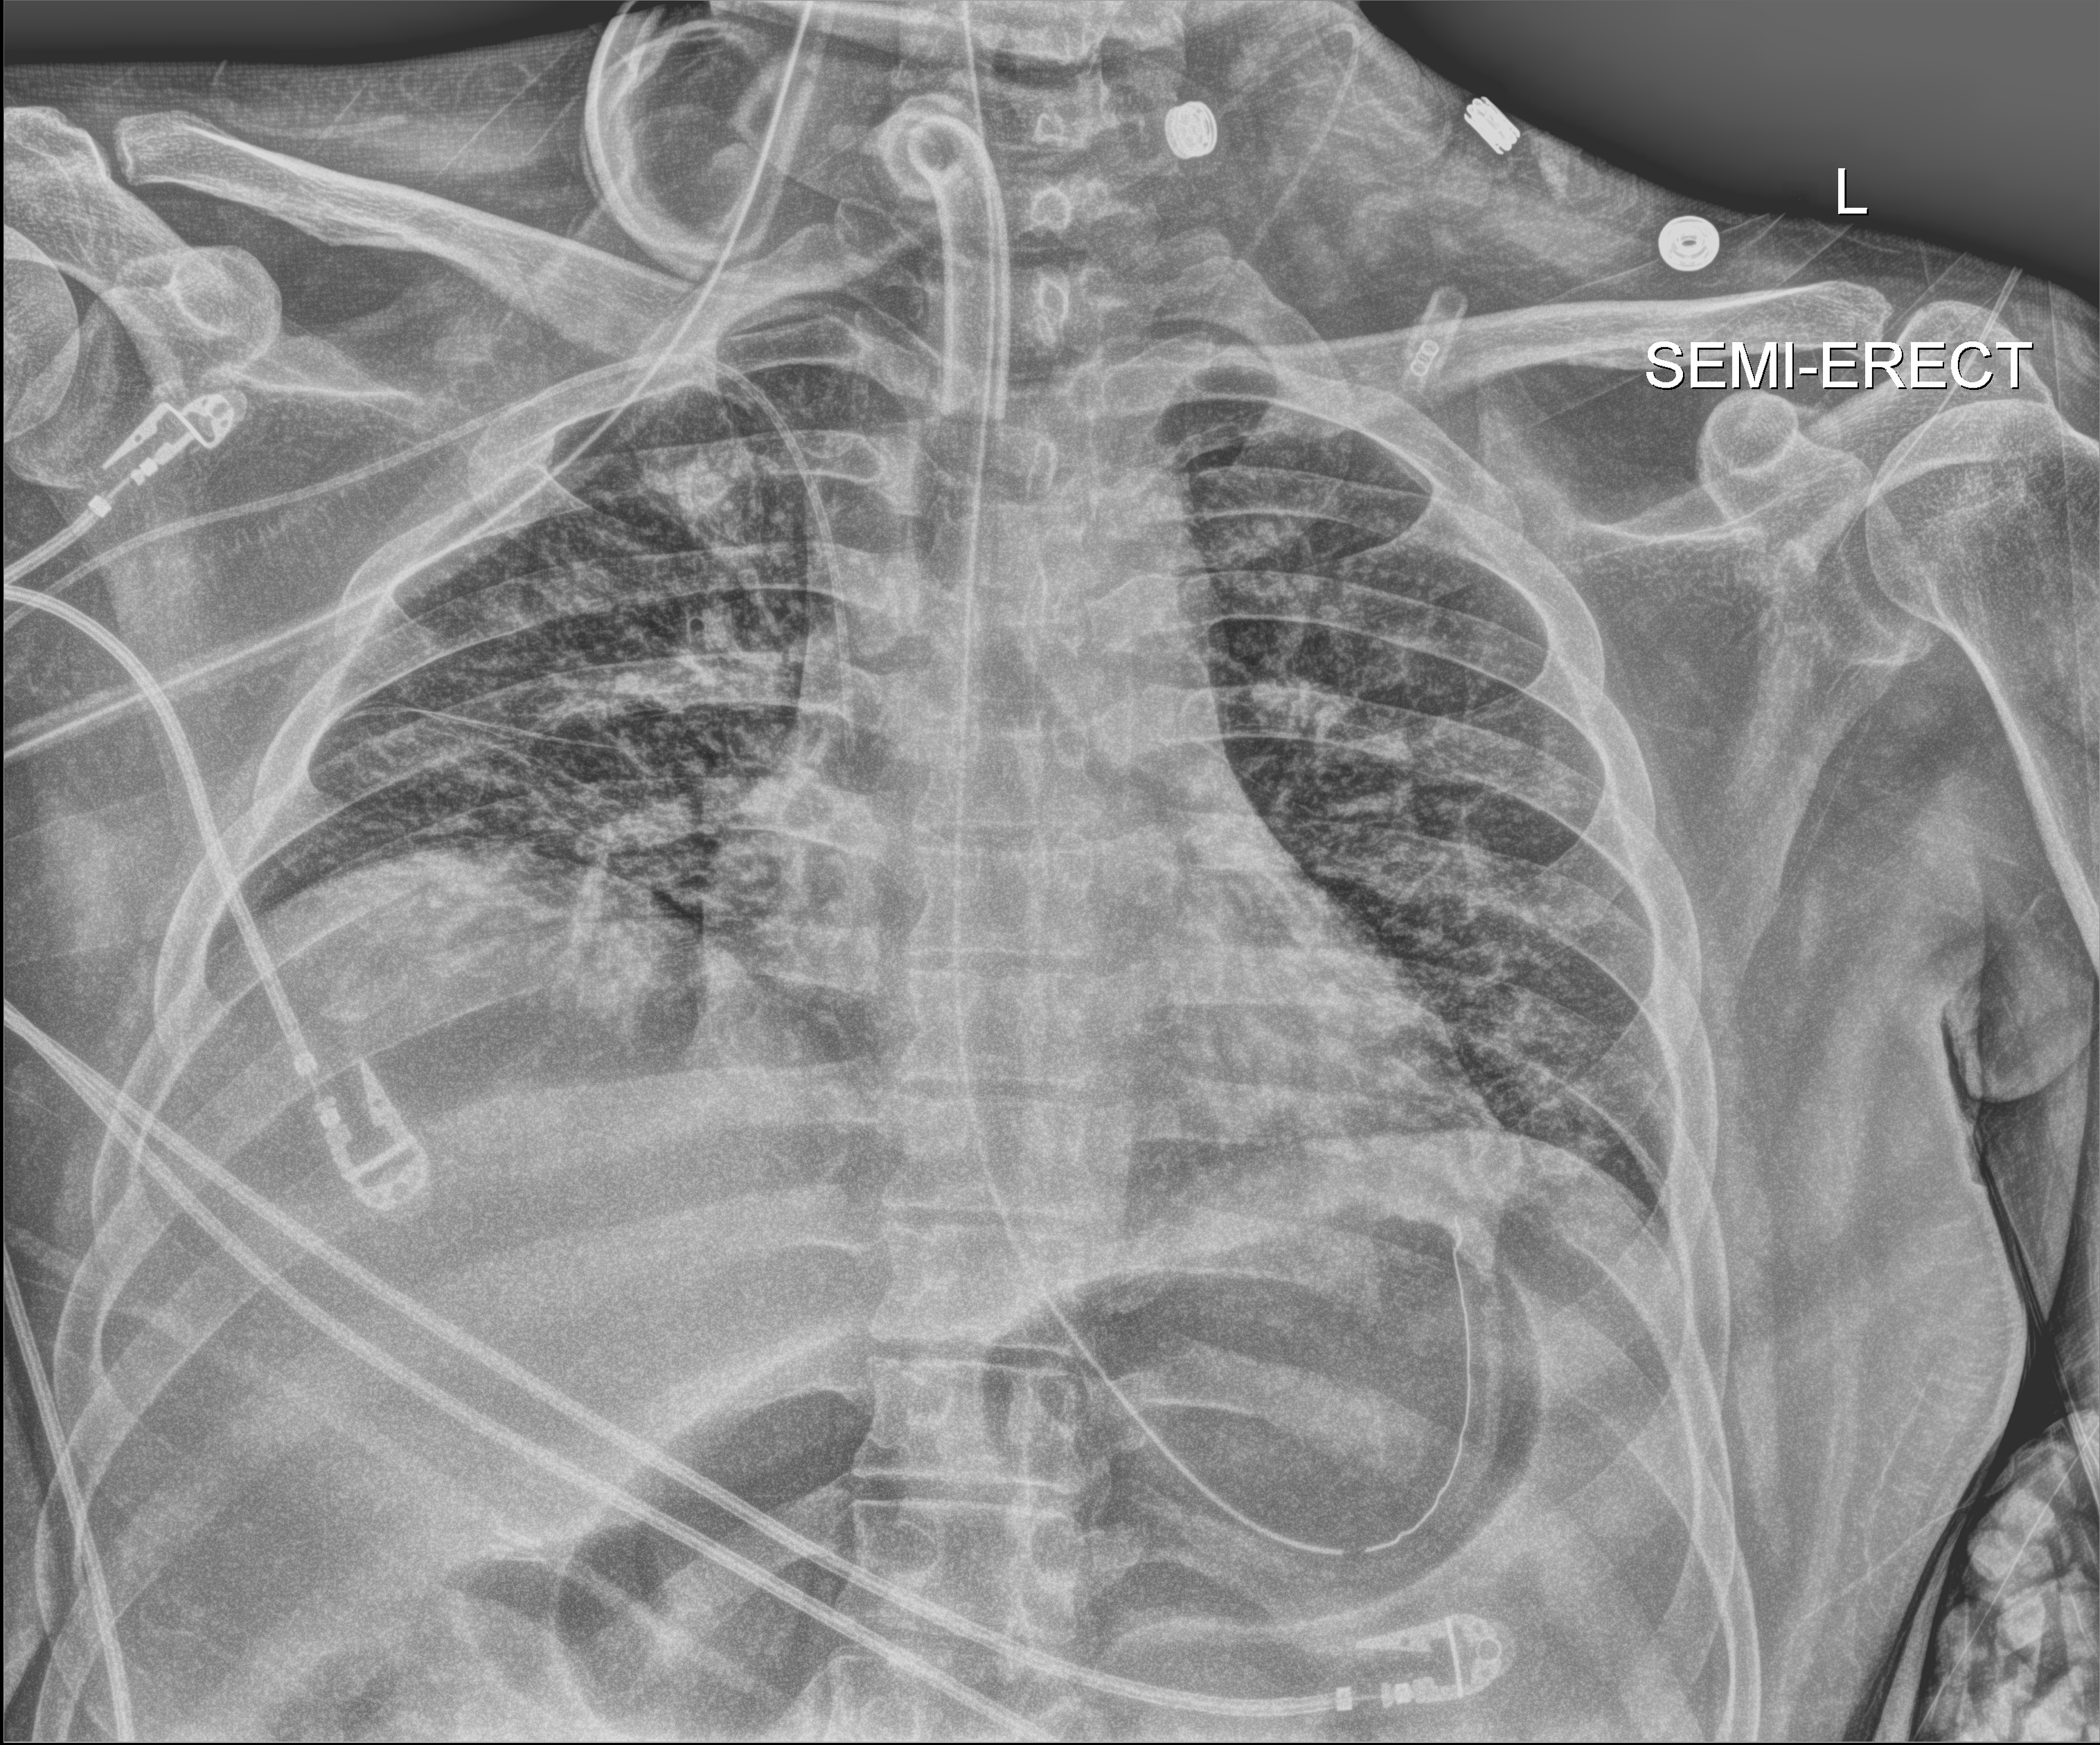
Chest X-ray (portable); anteroposterior (AP) projection. Male patient hospitalised with COVID-19, age 18–59 years.
Admission-level facts for this patient (not findings on this image; timing relative to this image not recorded): mechanically ventilated during this hospital stay: yes.